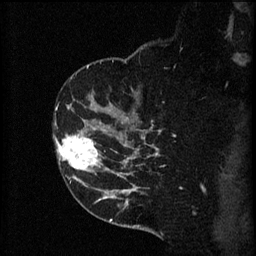
Breast MRI (dynamic contrast-enhanced), one sagittal slice; position 41 of 60 along the scan axis; 3 images stored at this slice position (order not interpretable as contrast timing); 1.5 T; TE 4.2 ms, TR 8.2 ms; 2 mm slice thickness; 256 × 256 image matrix. Patient: female, 49 years.
Structures marked on this image (semi-automatically segmented with operator editing):
- analysis volume of interest (the breast-tissue region the enhancement analysis was run in; not a lesion): bounding box [x1, y1, x2, y2] px = [55, 126, 105, 173]
- tumour enhancement mask (voxels above the 70 % enhancement threshold inside the analysis volume of interest): [56, 132, 101, 171]